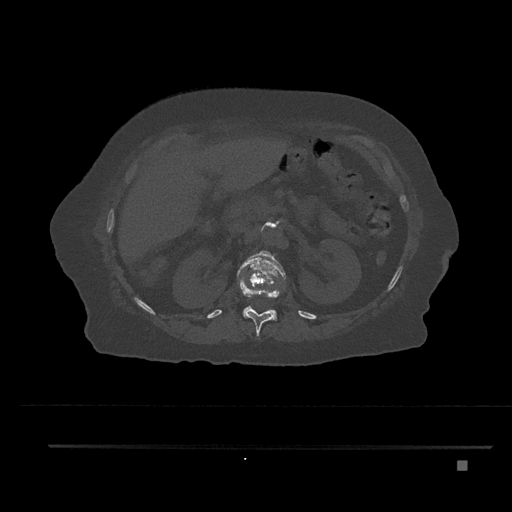
CT including the spine, one axial slice; position 245 of 797 along the scan axis; reconstruction kernel Br40s/3; 120 kVp; bone window (W 1800 / L 400 HU); 0.5 mm slice thickness; 512 × 512 image matrix, field of view 437 × 437 mm. Female patient, age 76 years. Case-level facts recorded for this patient, not image findings: primary cancer: lung; vertebrae with lytic lesions (as recorded): T11, L3.
Outlined on this slice (semi-automatically segmented with operator editing):
- L1 vertebra: bounding box [x1, y1, x2, y2] px = [237, 251, 286, 320]
- T12 vertebra: [239, 274, 281, 336]